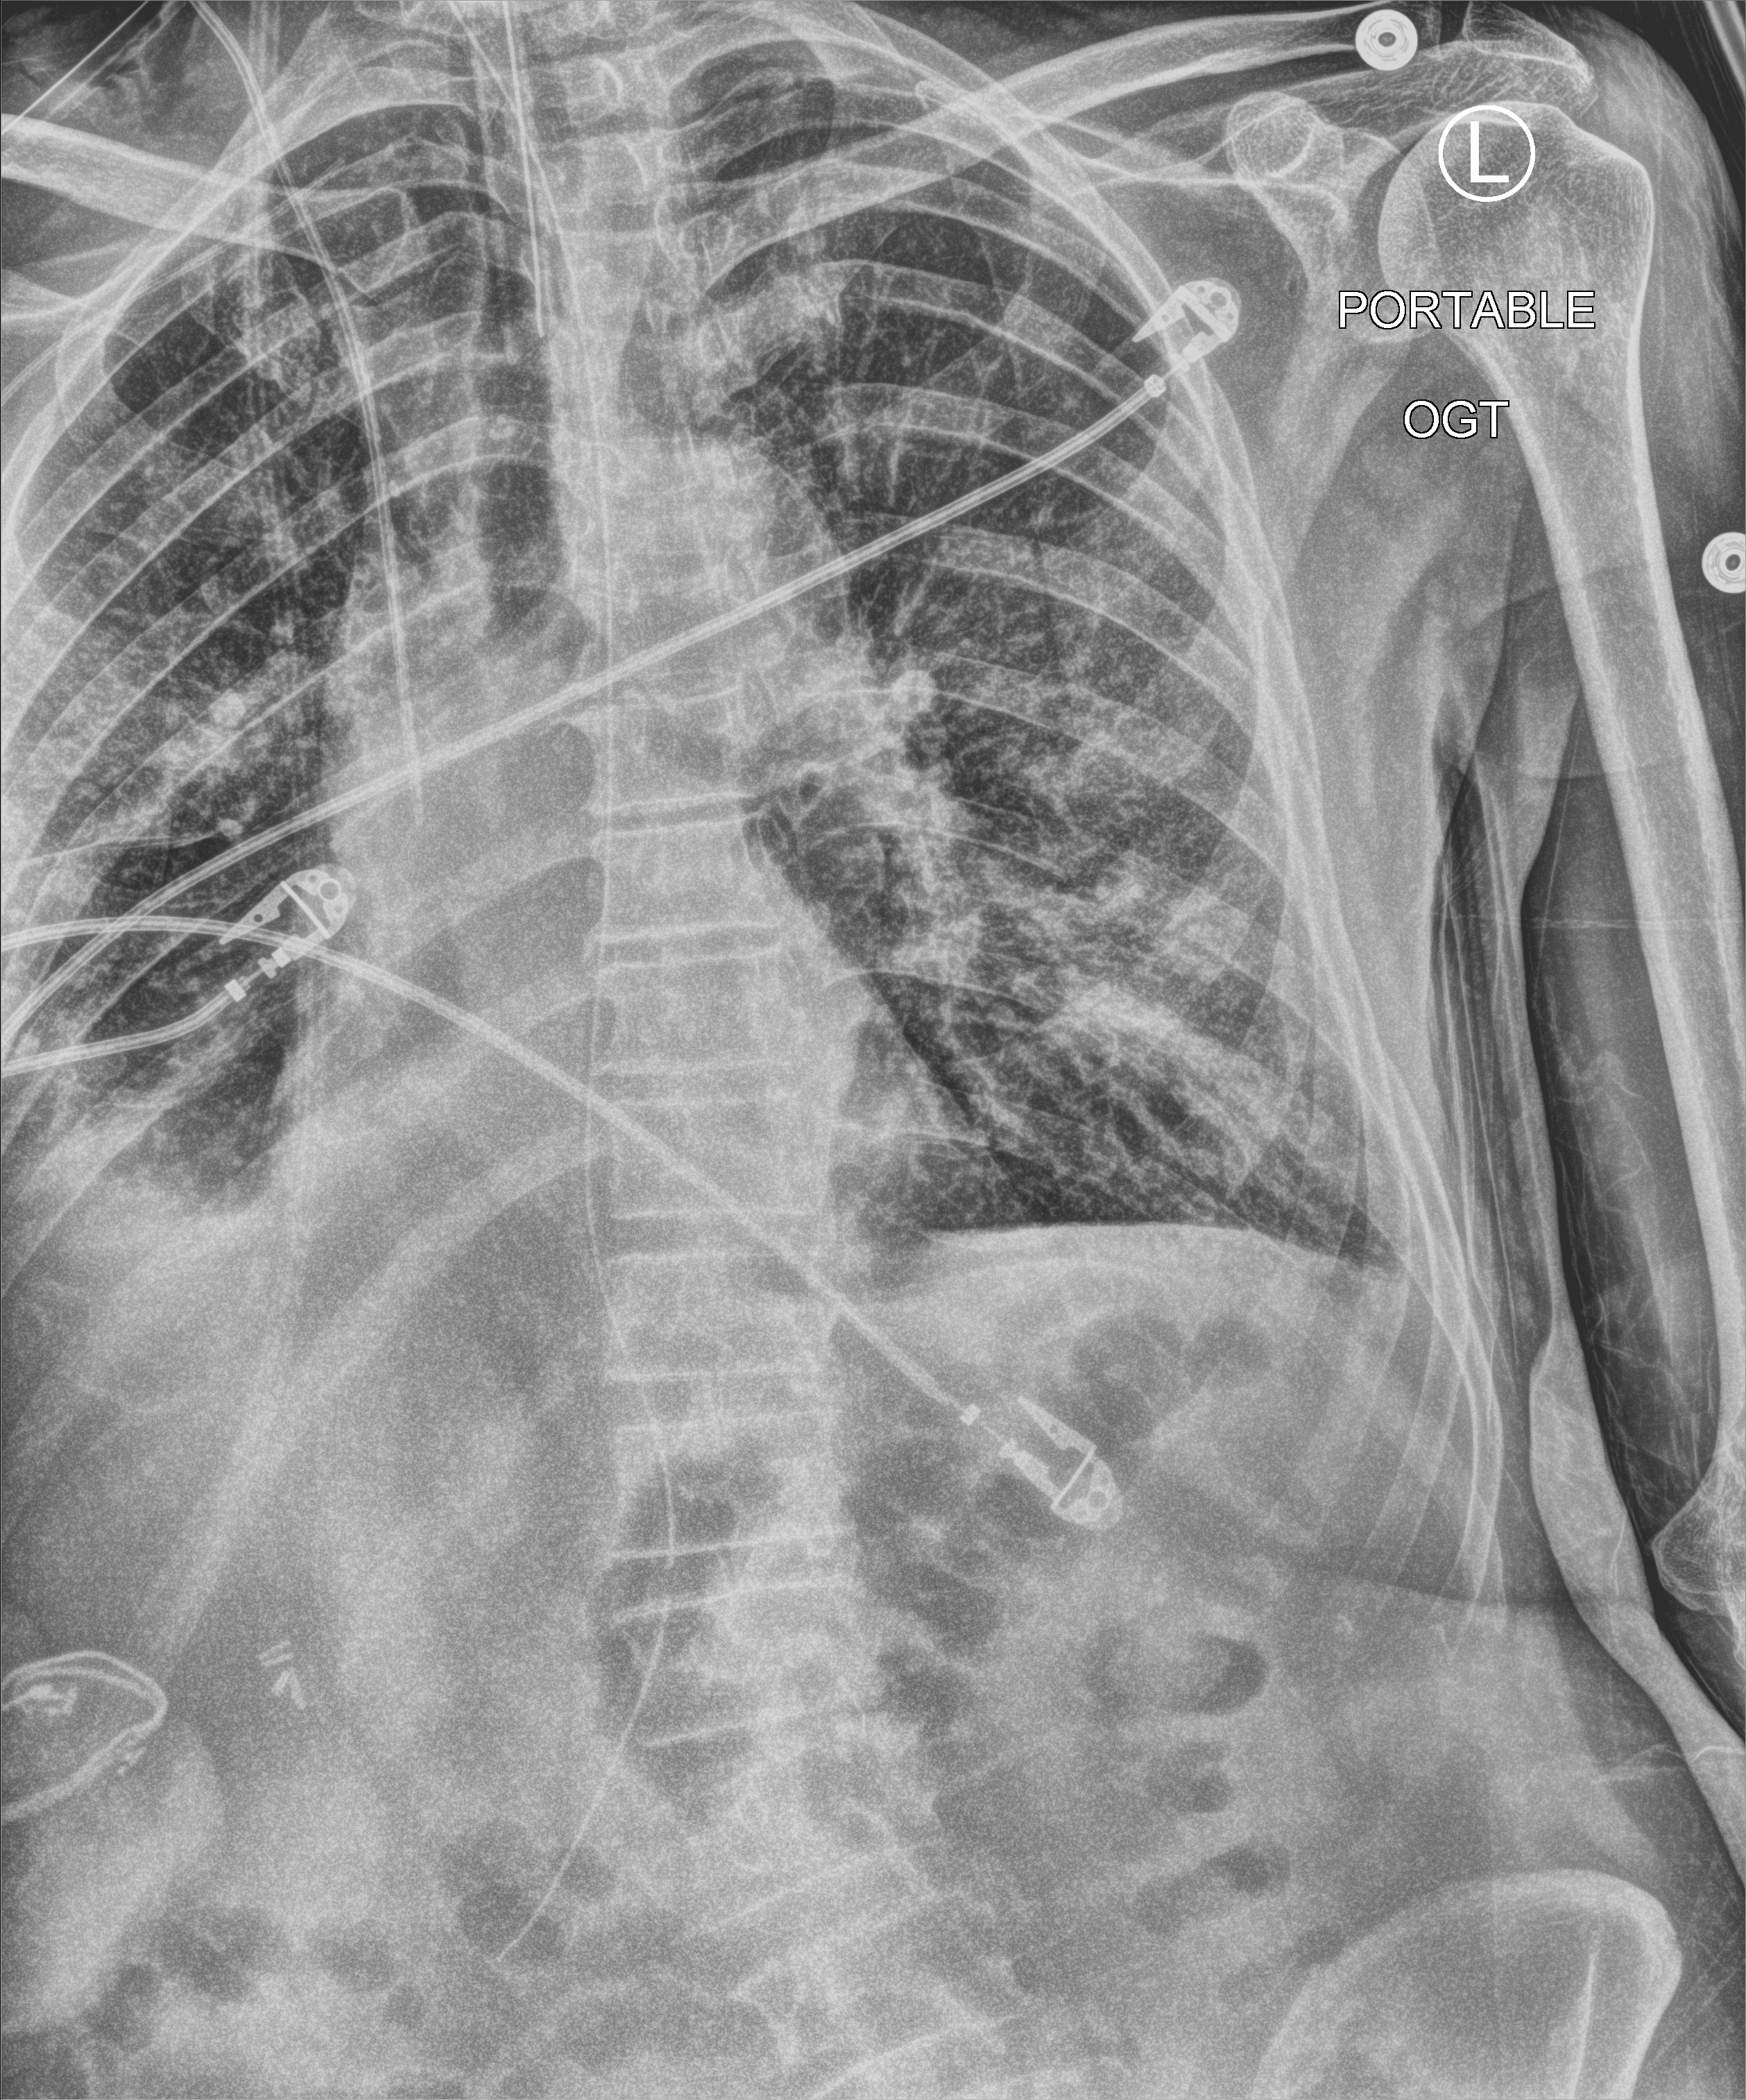
Chest X-ray (portable); anteroposterior (AP) projection. Male patient hospitalised with COVID-19, age 75–90 years.
From the hospital-stay record, not from the radiograph (when in the stay this image was taken is not recorded): admitted to intensive care during this hospital stay: yes.